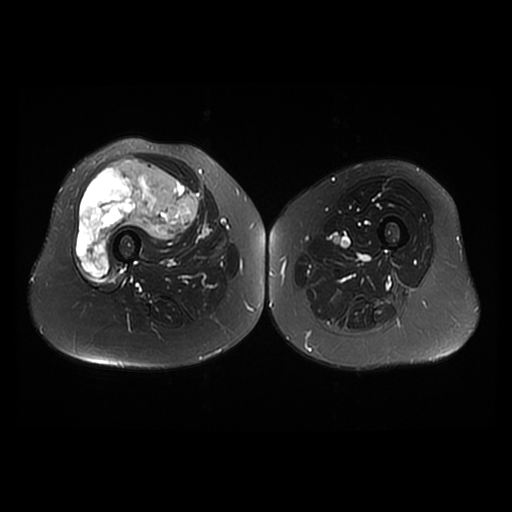
MRI of an extremity soft-tissue mass, one axial slice; position 20 of 42 along the scan axis; T2-weighted fat-saturated; 512 × 512 image matrix, field of view 440 × 440 mm. Female patient. From the clinical record (not read from this slice): histological type: pleiomorphic undifferentiated sarcoma; grade: high; site of the primary tumour: right quadricep.
Annotated regions visible in this slice (manually delineated by an expert):
- gross tumour volume including surrounding oedema: bounding box <76,156,199,277> (left, top, right, bottom; pixels)
- gross tumour volume (mass): <76,156,199,277>